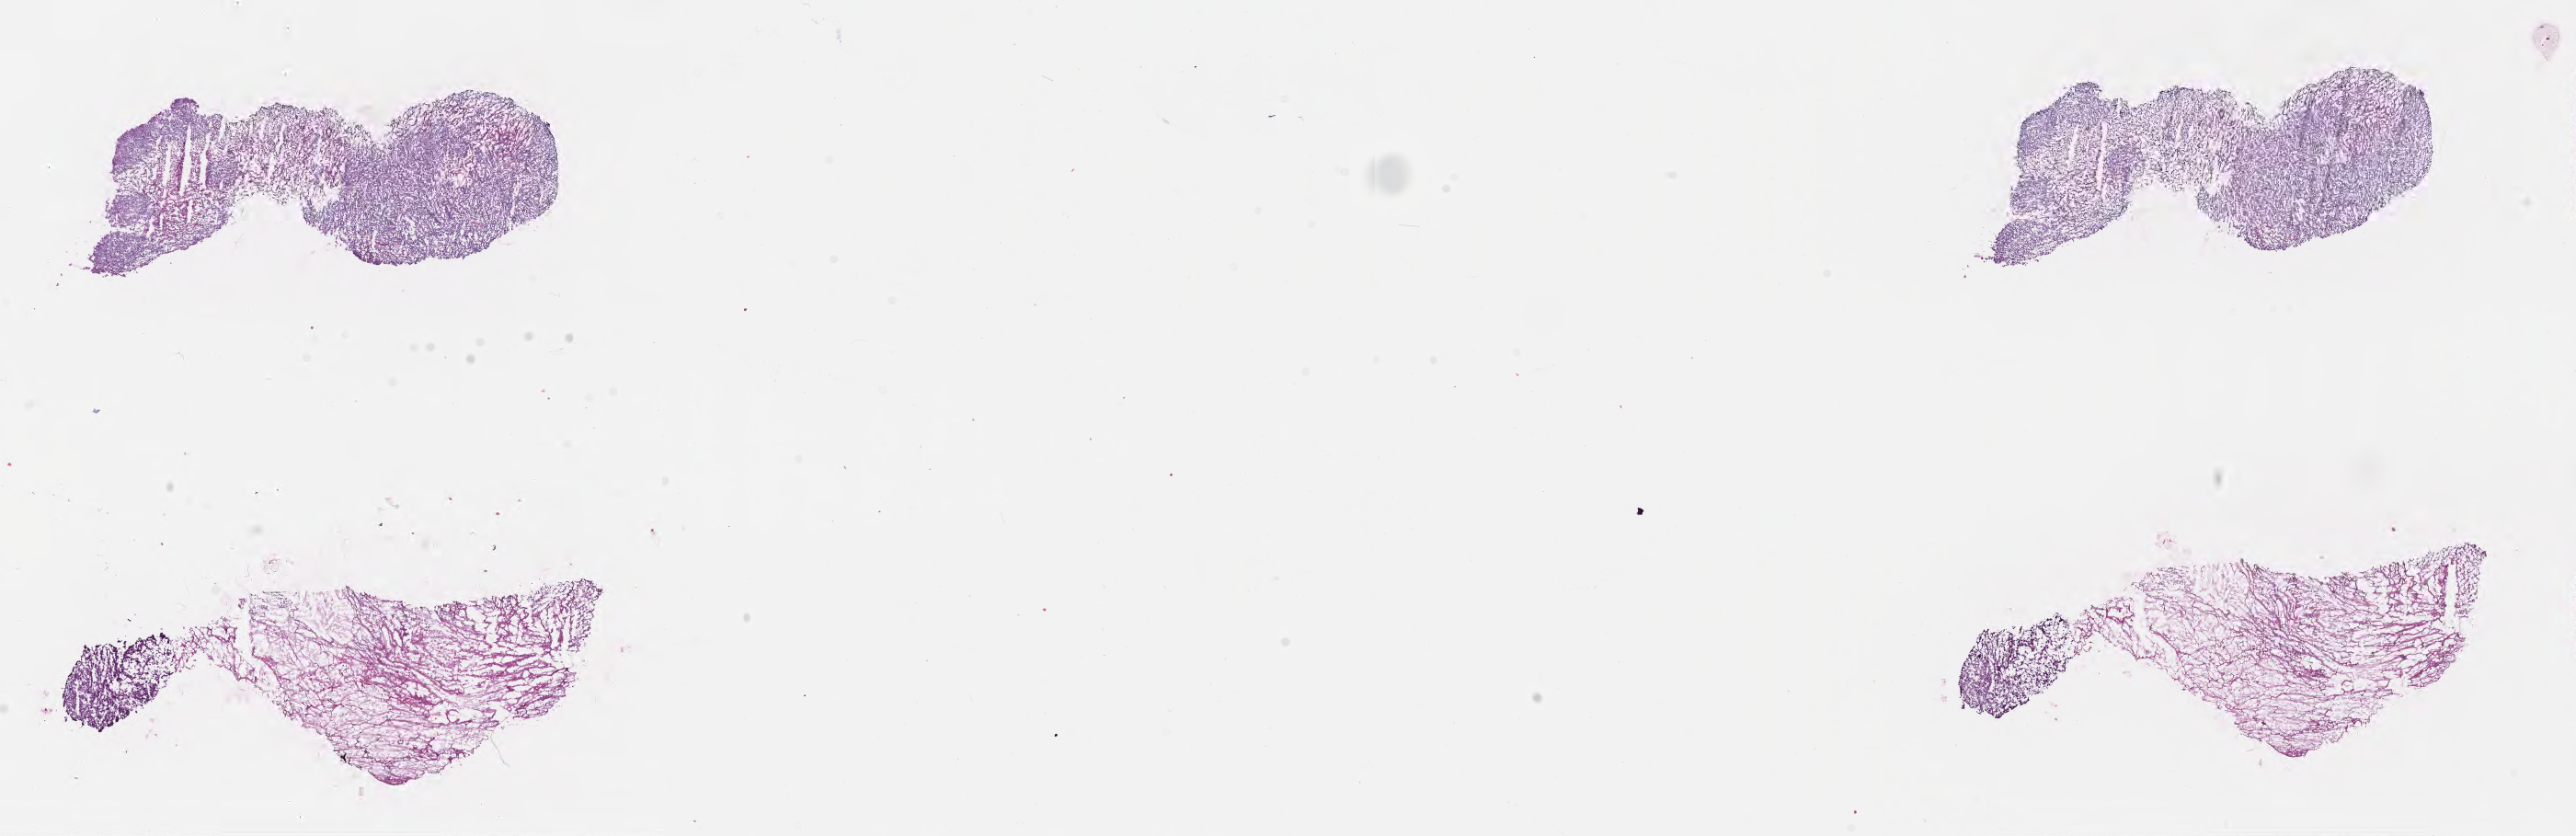
Digitized H&E-stained section, shown as a low-resolution overview of the whole scanned area (about 22.6 x 7.3 mm), frozen section, specimen: metastatic tumor tissue, resected from brain. Male, age 9 years at initial diagnosis. Composition of this section per pathologist review: tumor cells 50%, tumor nuclei 90%, stromal cells 40%, necrosis 10%, normal cells 0%. Infiltration values recorded for this section: lymphocyte infiltration 0%, monocyte infiltration 0%, neutrophil infiltration 0%.
Section: top of the tissue portion. Patient diagnosis (primary): Undifferentiated sarcoma.